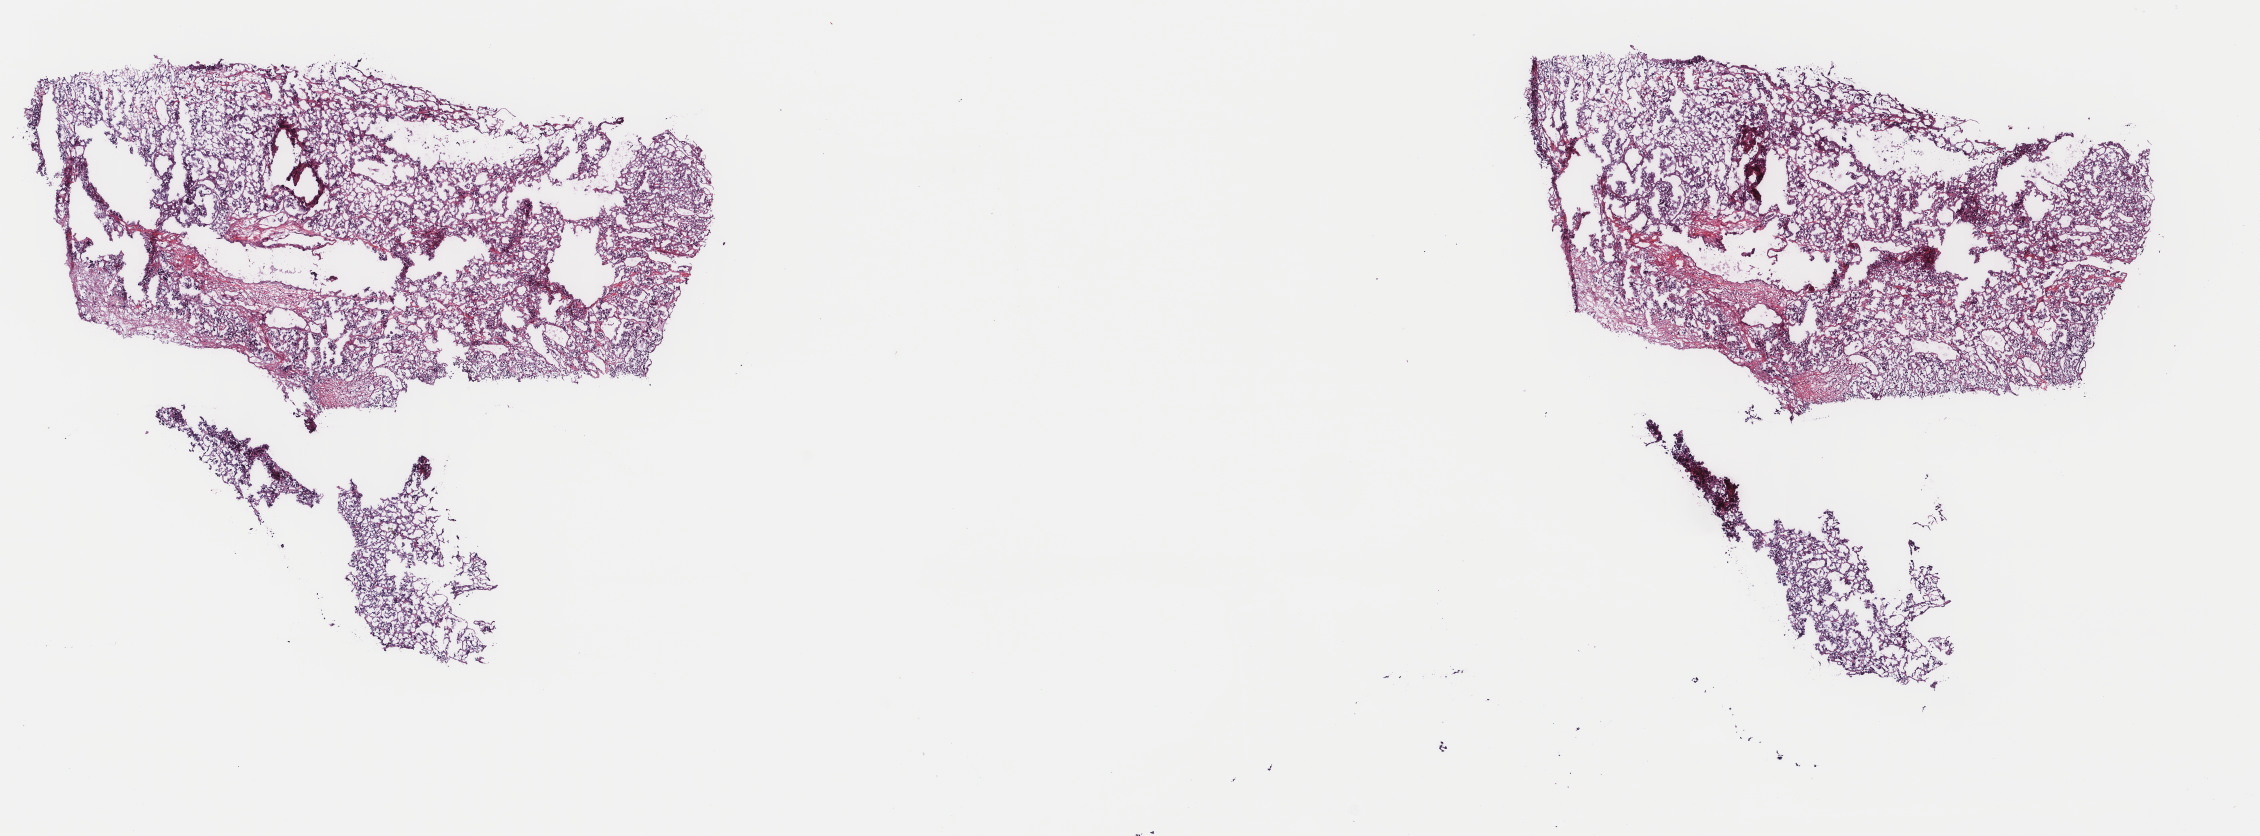
H&E-stained whole-slide image, low-resolution overview of the scanned area, about 17.9 x 6.6 mm; frozen section from the top of the tissue portion; primary tumour sample from the adrenal gland. Male, age 23 years at initial diagnosis. Slide review estimates, as recorded: tumour cells 90%, tumour nuclei 90%, normal cells 0%, stromal cells 10%, necrosis 0%. Infiltration values recorded for this section: lymphocyte infiltration 0%, monocyte infiltration 0%, neutrophil infiltration 0%.
* laterality: right
* diagnosis: Pheochromocytoma, NOS